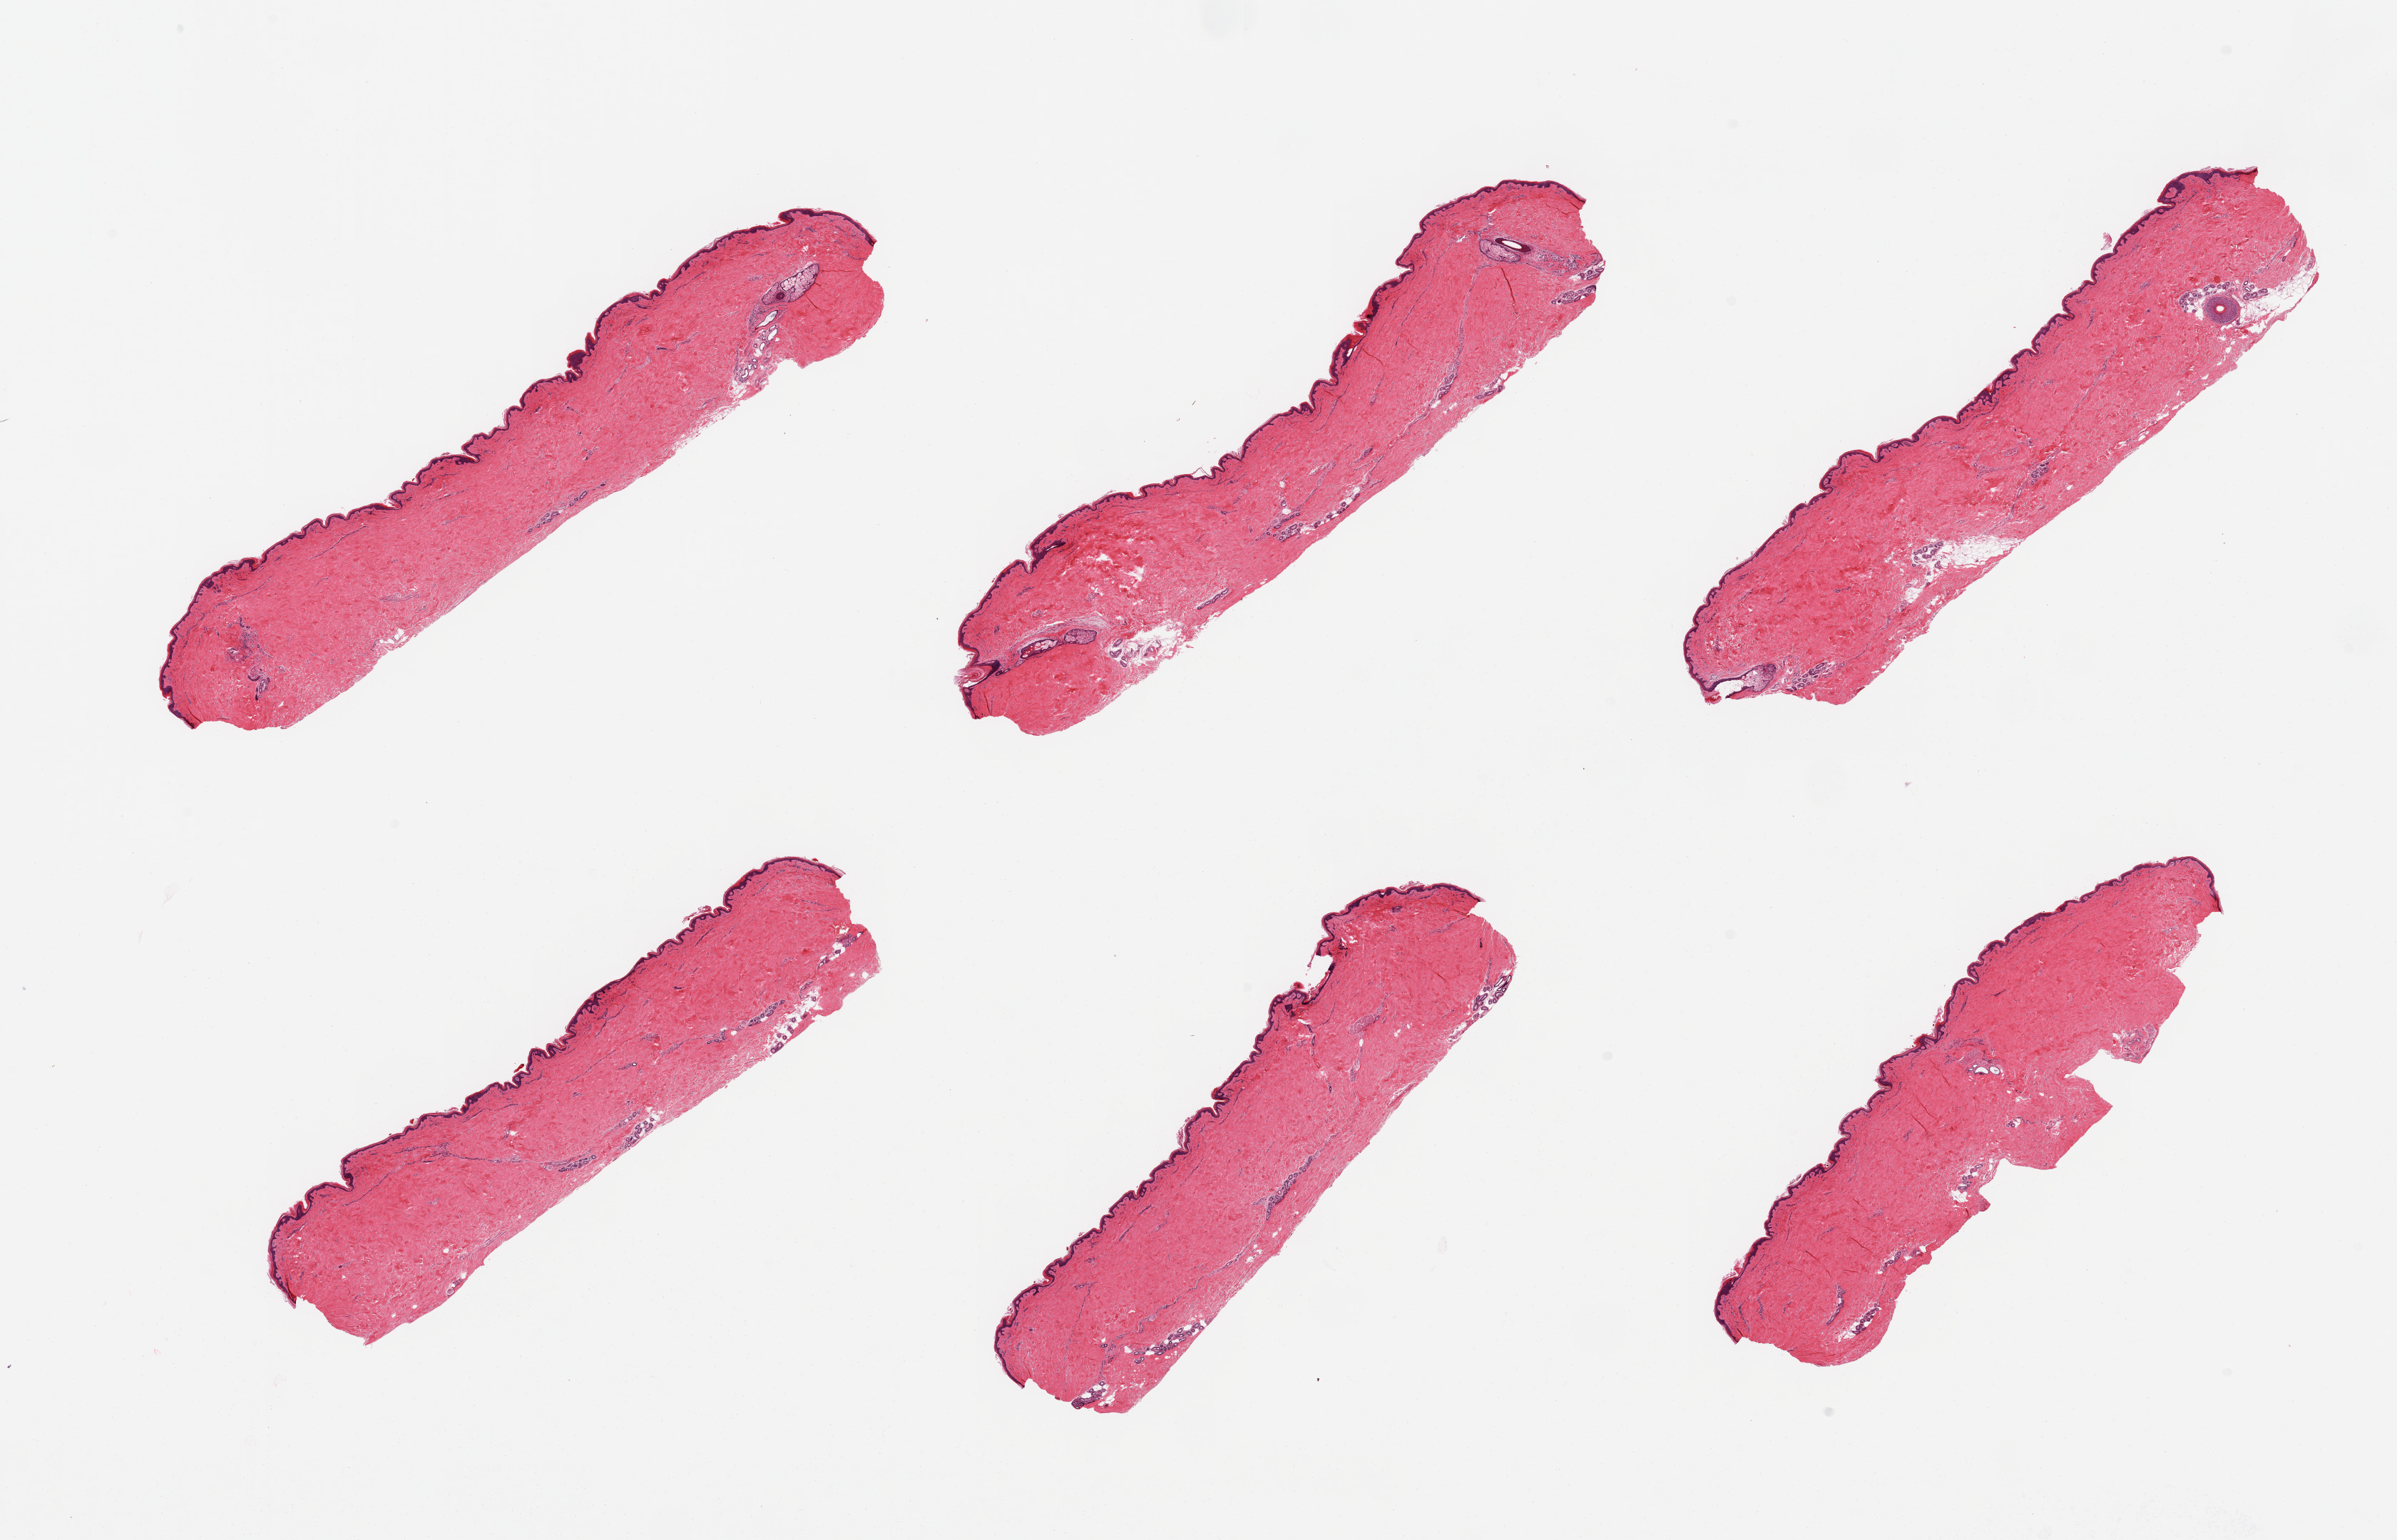
Digitized H&E-stained section — a low-resolution overview of the entire scanned area, about 26.6 x 17.1 mm (acquisition: 20x scan); PAXgene-fixed, paraffin-embedded tissue; section of skin of suprapubic region (target tissue); donor tissue sample. Donor sex: male.
Reviewer comment on this tissue sample: 6 pieces; well trimmed with minimal internal fat.